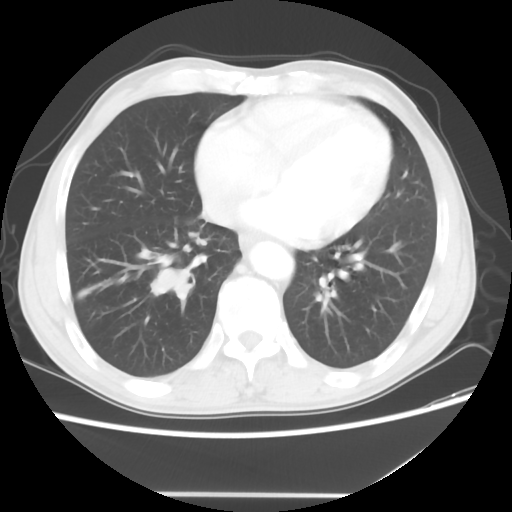
Chest CT, one axial slice; slice 17 of 56 in the series (ordered by position); 120 kVp; lung window (W 1500 / L -600 HU); 5 mm slice thickness; 512 × 512 image matrix, field of view 344 × 344 mm. Patient: male, 65 years. Case-level facts recorded for this patient, not image findings: clinical TNM (as recorded): T1c N3 M0.
Annotated regions visible in this slice (rectangle marked by the reading radiologist):
- lung tumour (recorded histology: small cell carcinoma): bounding box <139,245,196,306> (left, top, right, bottom; pixels)